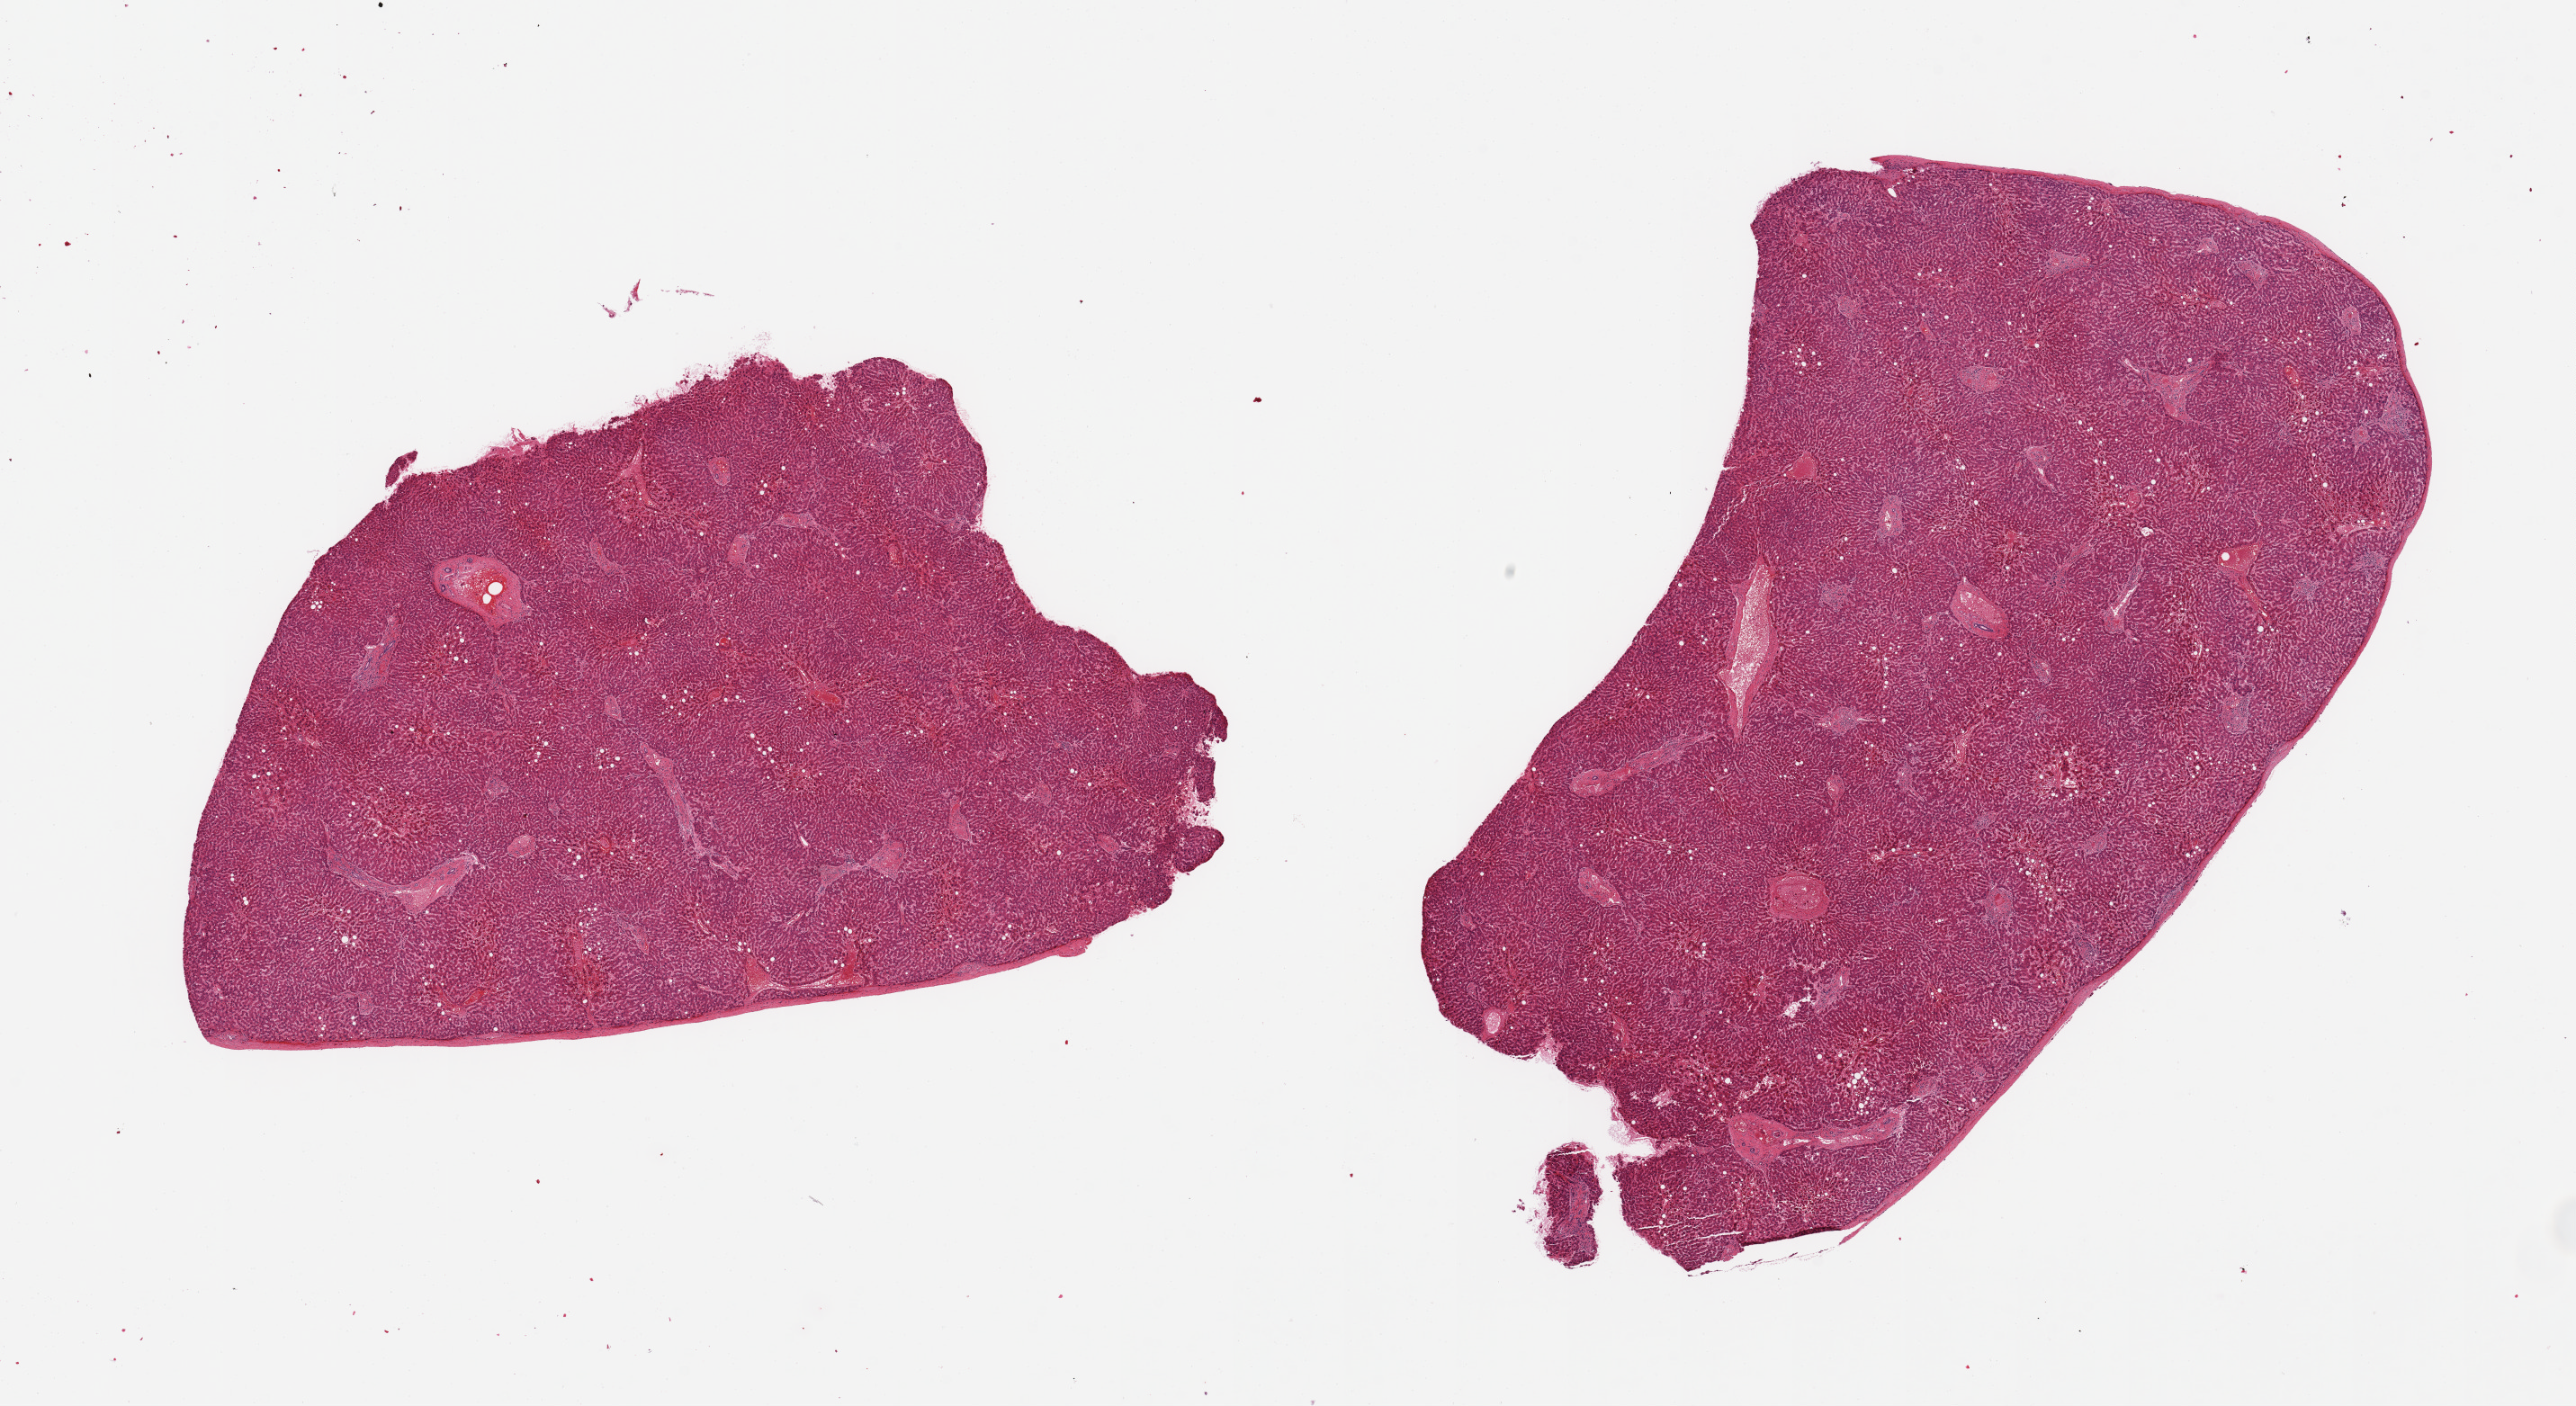
Whole-slide image, haematoxylin and eosin stain — a low-resolution overview of the entire scanned area, about 22.6 x 12.4 mm; PAXgene-fixed, paraffin-embedded tissue; target tissue: liver; tissue donor sample.
Pathologist's review note for this sample: 2 pieces; includes capsule (target is 1cm below capsule), mild steatosis and congestion.